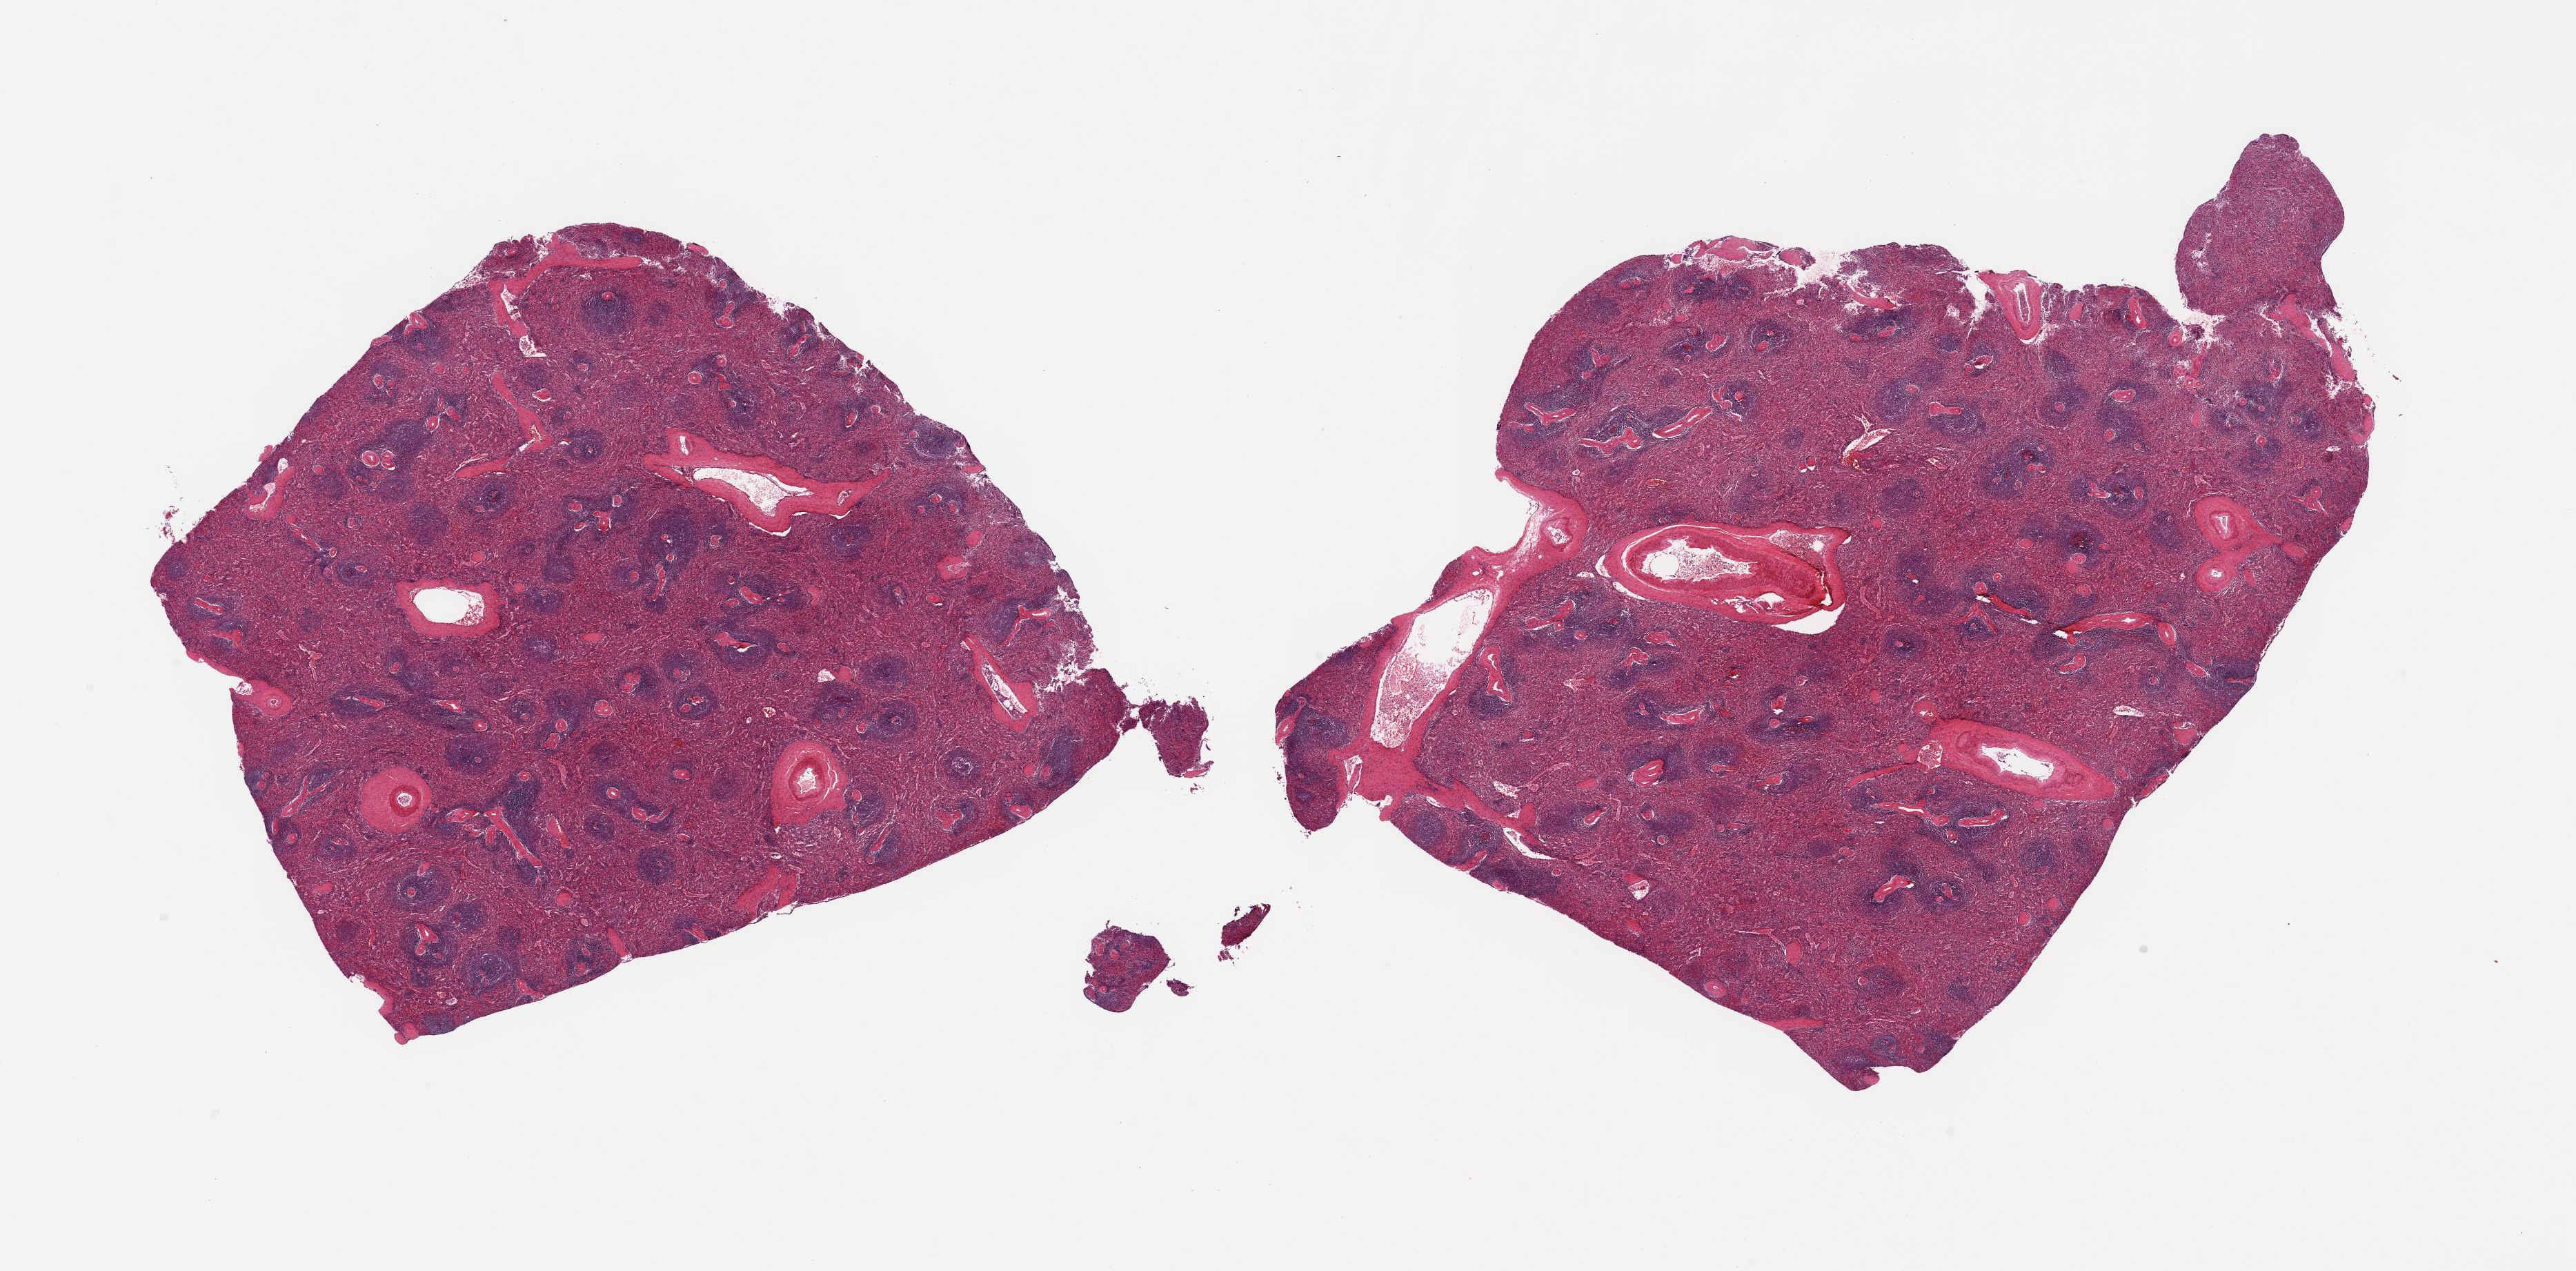
Digitized H&E-stained section, low-resolution overview of the scanned area, about 29.5 x 14.6 mm (acquisition: 20x scan); PAXgene-fixed paraffin-embedded (PFPE) section; target tissue: spleen; tissue donor sample. Female donor.
Reviewer comment on this tissue sample: 2 pieces, no abnormalities.